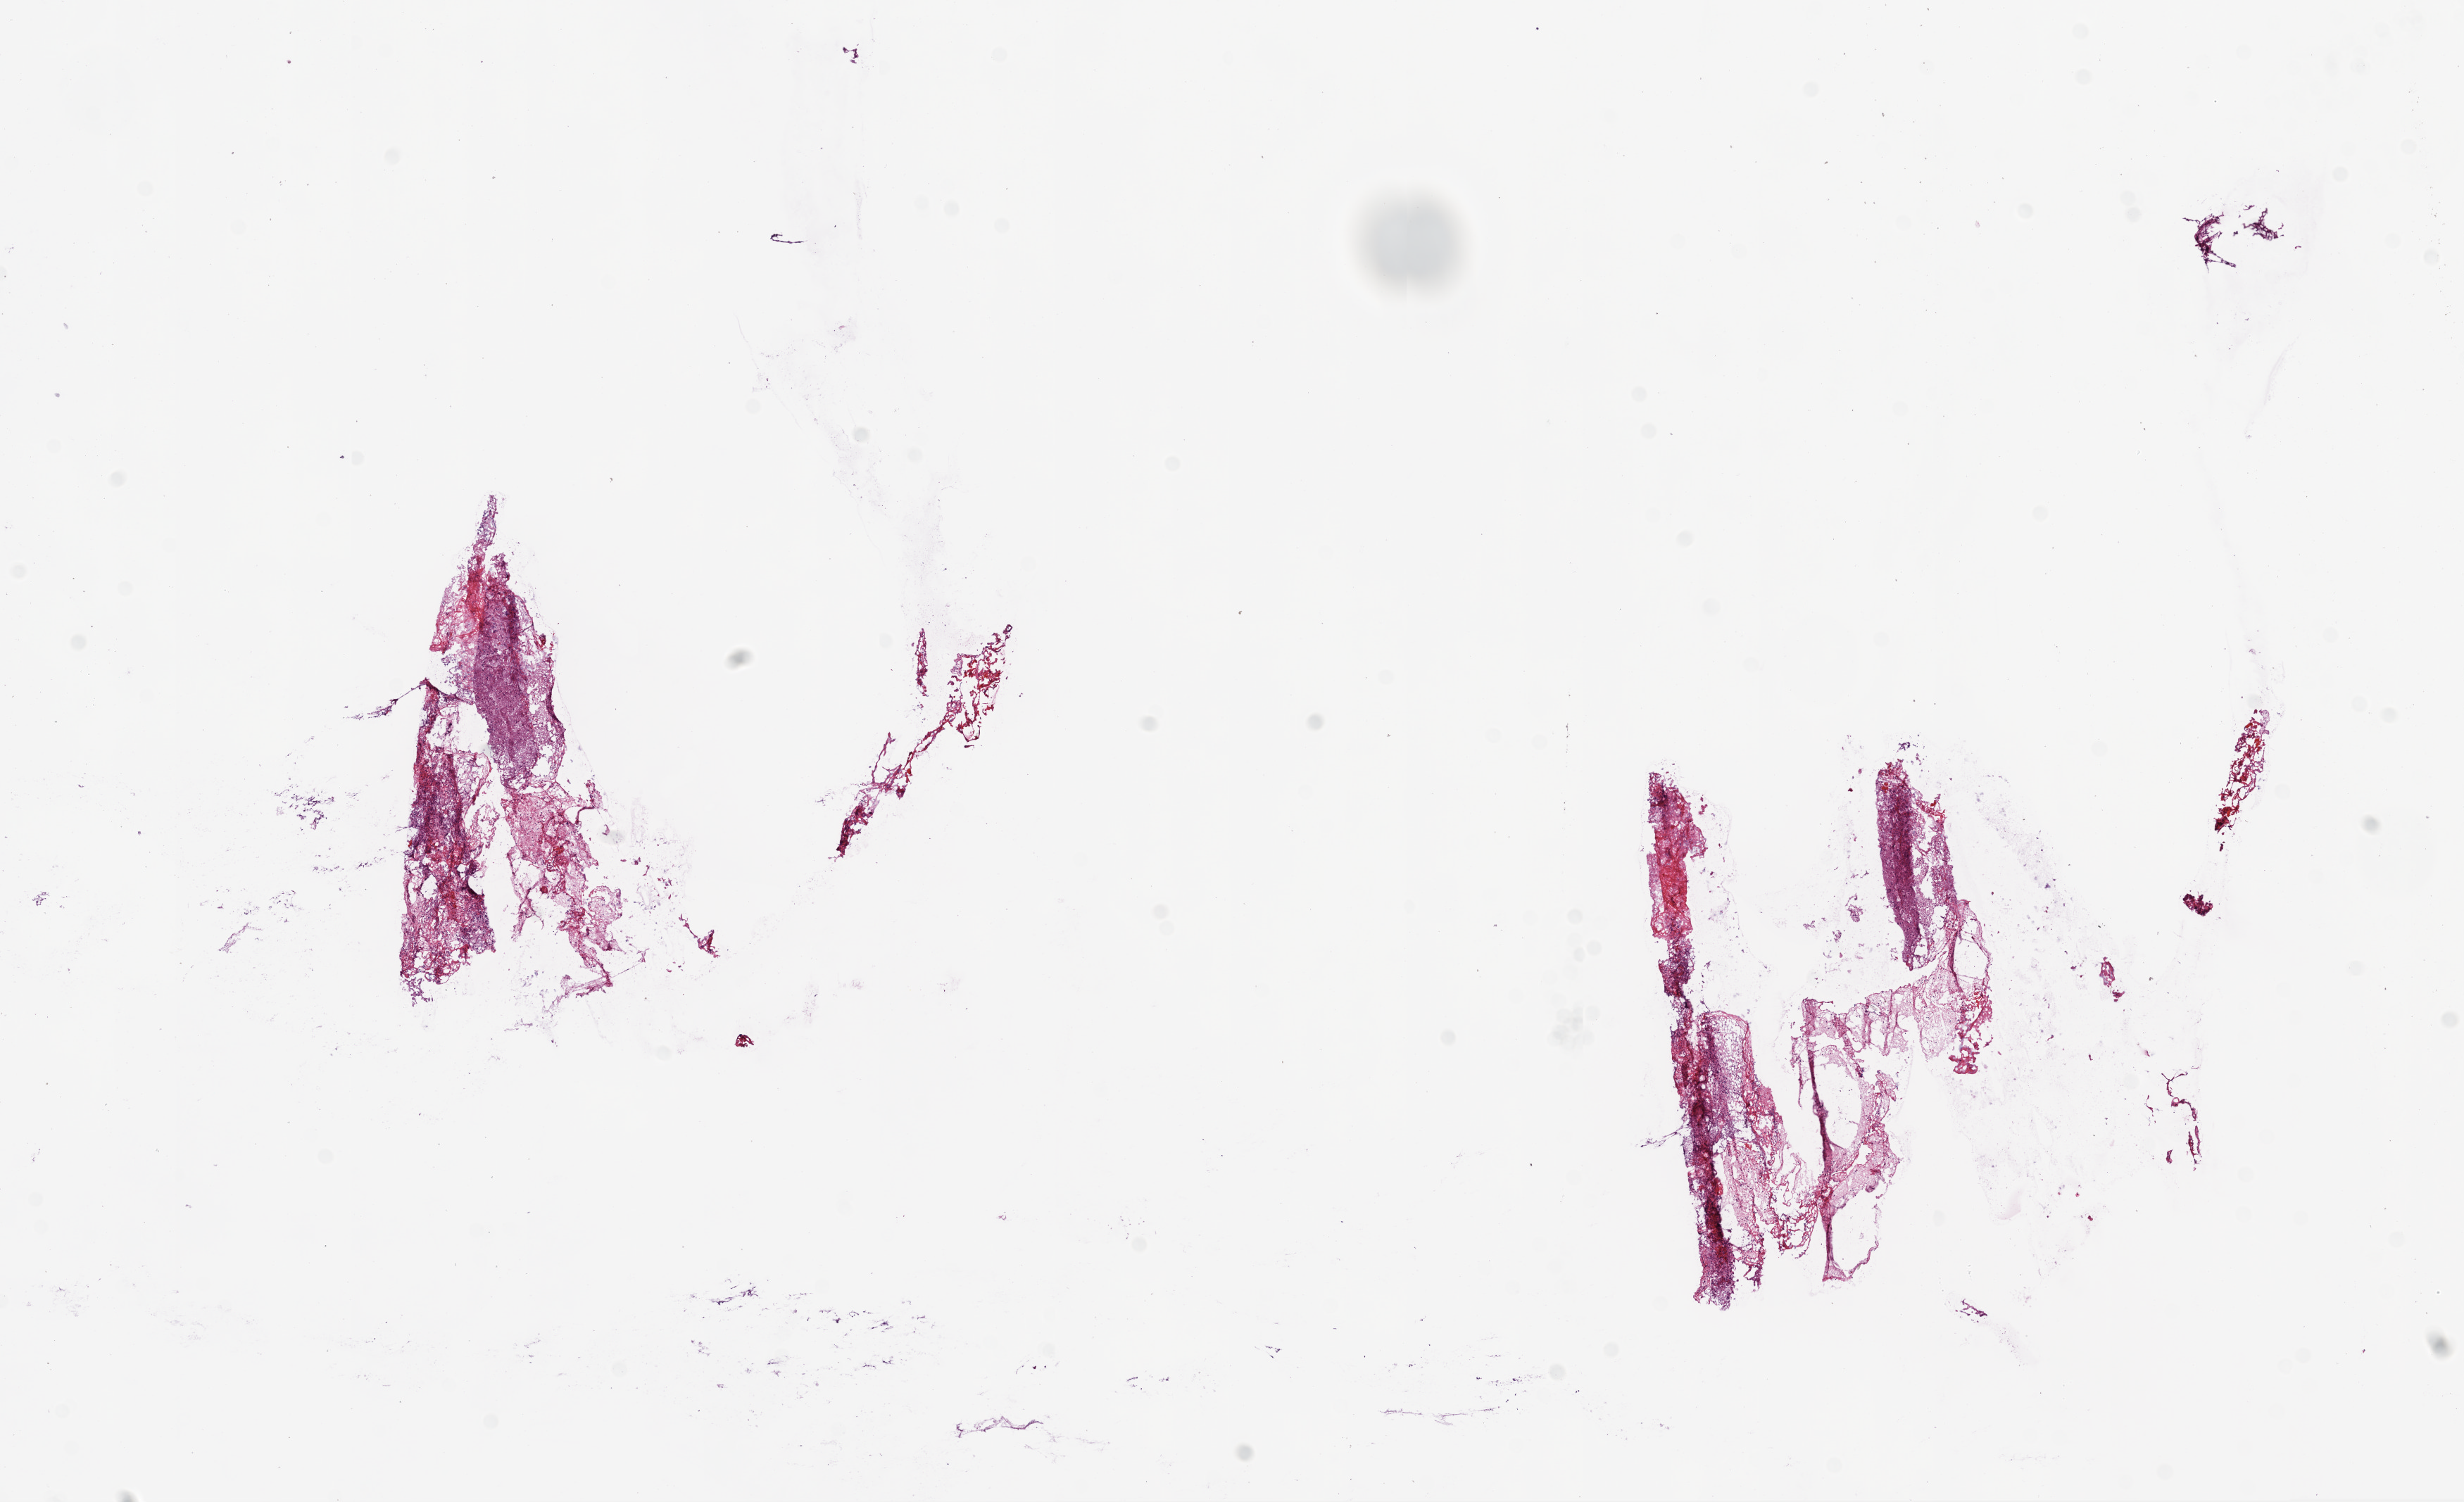
Whole-slide histology image, H&E, shown as a low-resolution overview of the whole scanned area (about 14.0 x 8.6 mm). Frozen section. Brain, primary tumour sample. Female patient; age at initial diagnosis 69 years. Slide review estimates, as recorded: tumour nuclei 0%, necrosis 0%.
• diagnosis: Glioblastoma